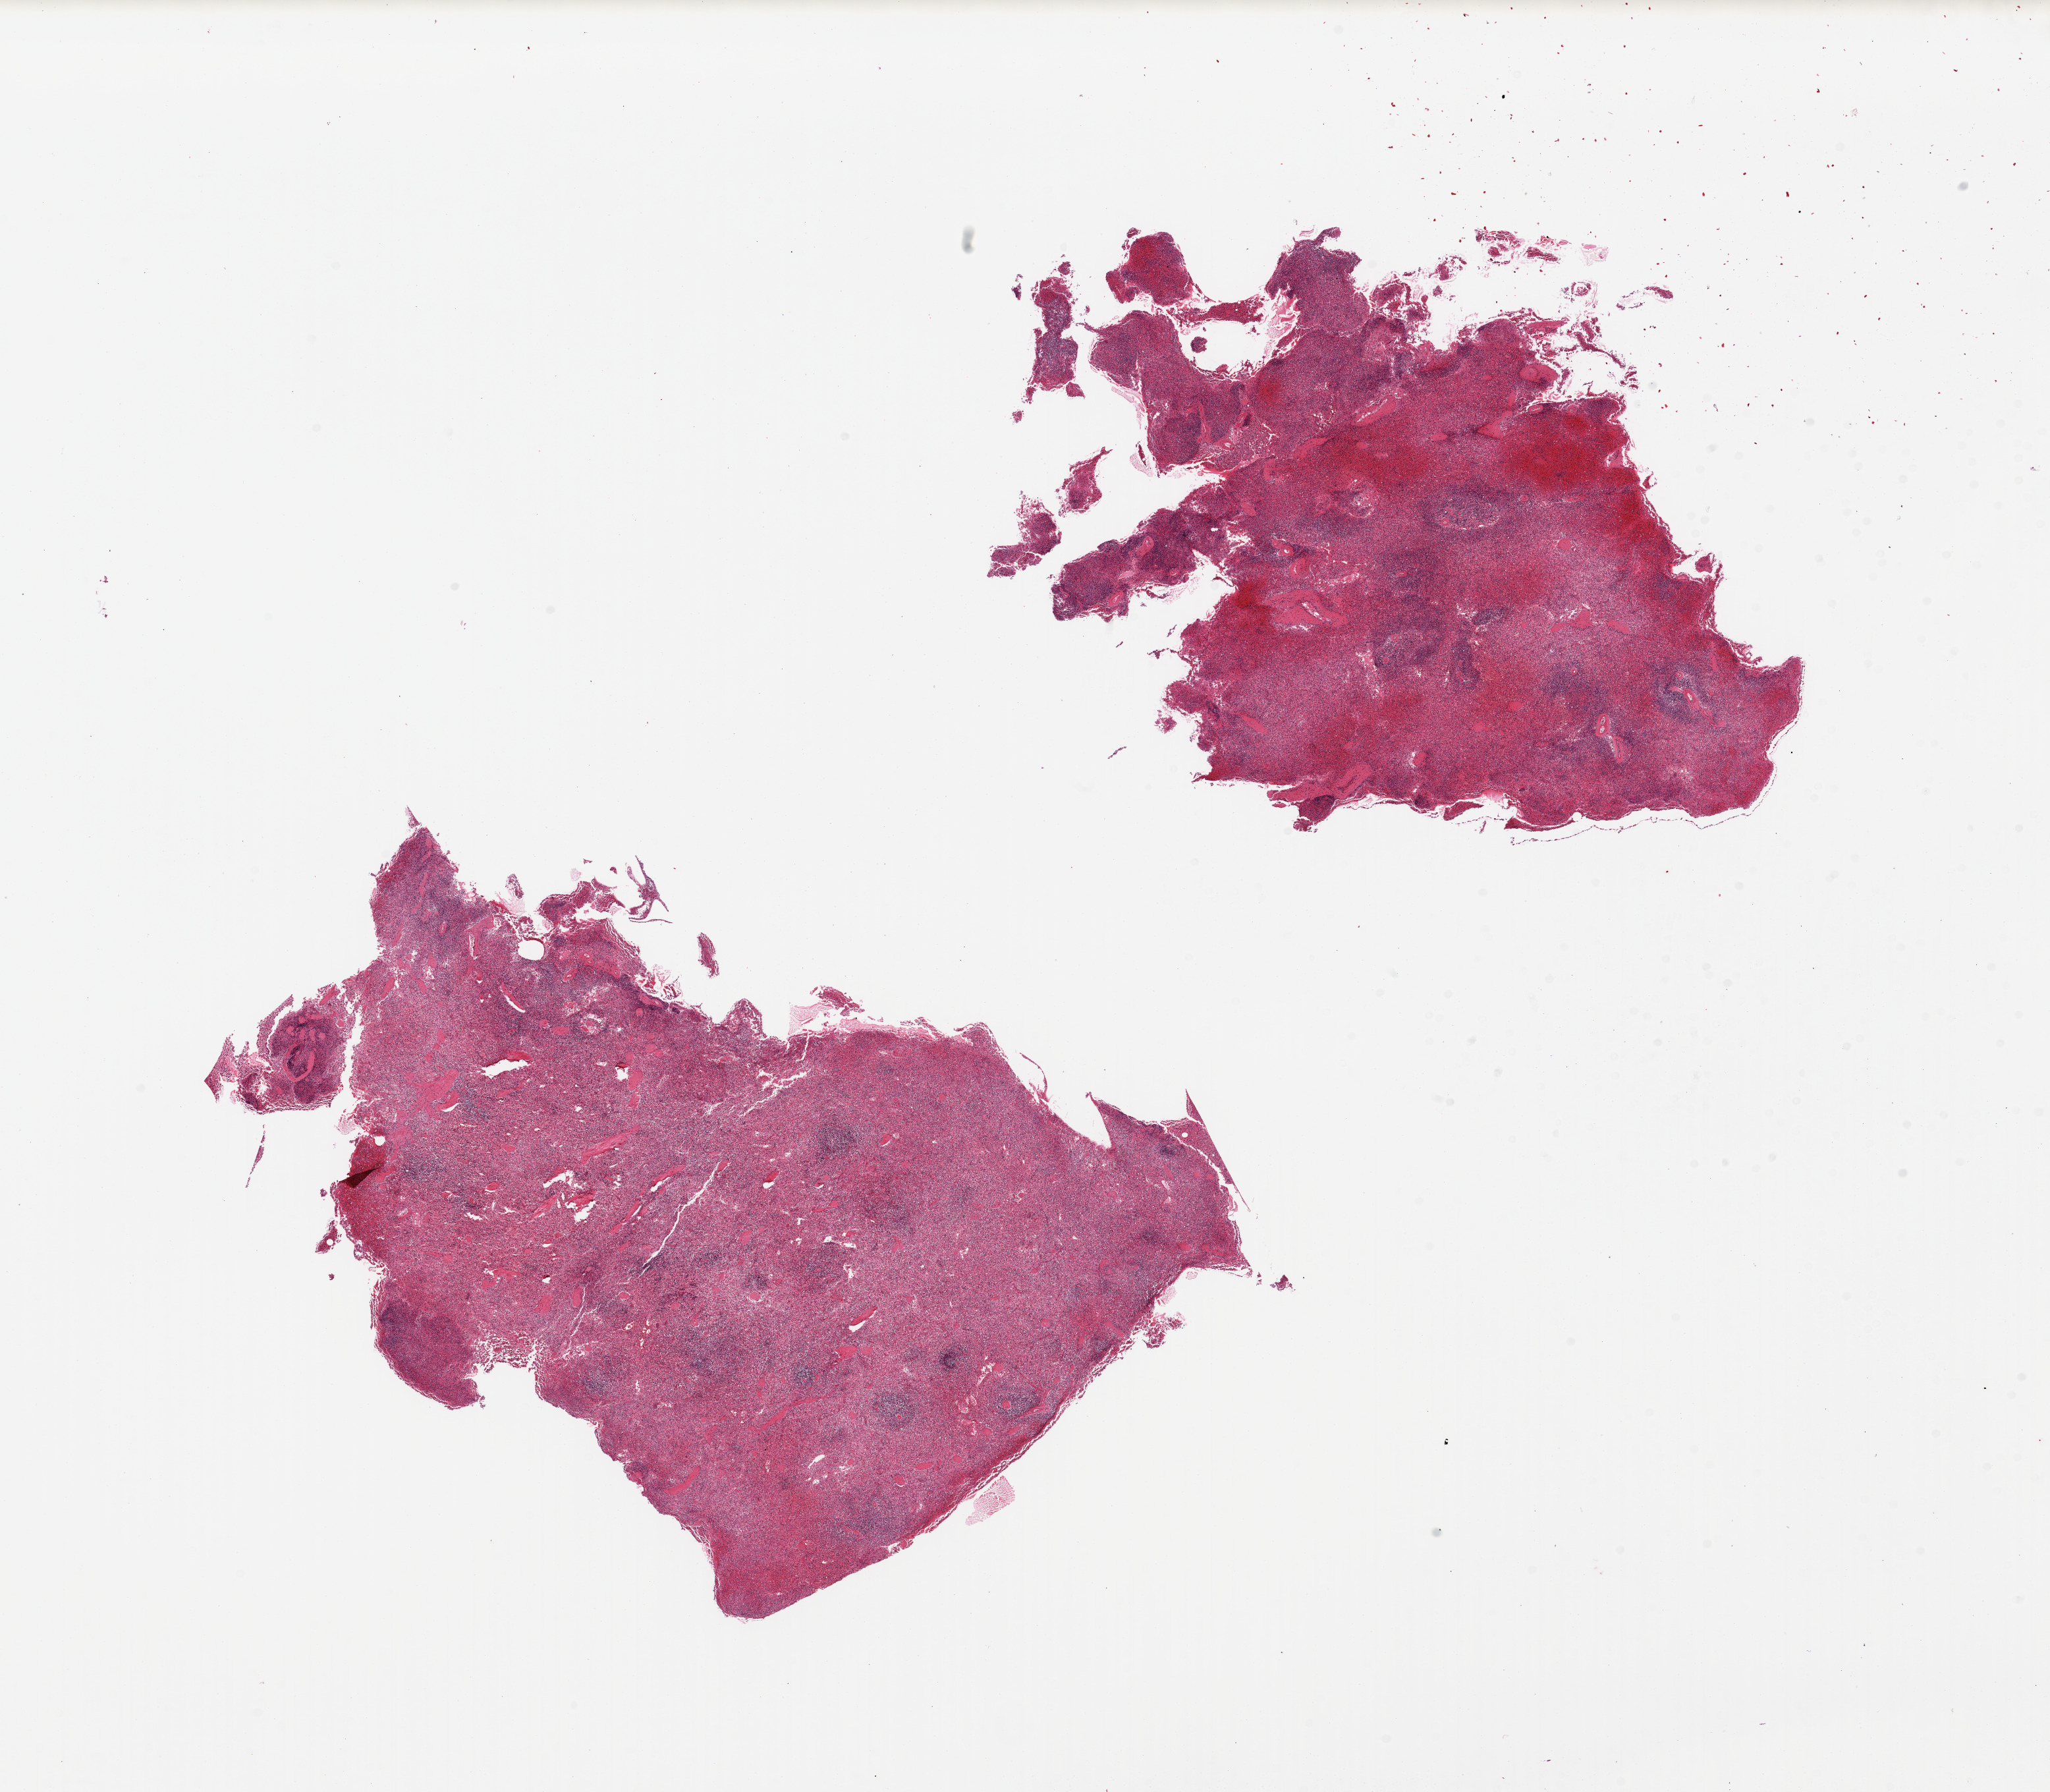
Digitized haematoxylin and eosin-stained section, whole scanned area (about 24.6 x 21.5 mm) shown as a low-resolution overview, PAXgene-fixed, paraffin-embedded tissue, target tissue: spleen, donor tissue sample. Donor: female.
* reviewer comment on this tissue sample: 2 pieces, congested, badly autolyzed